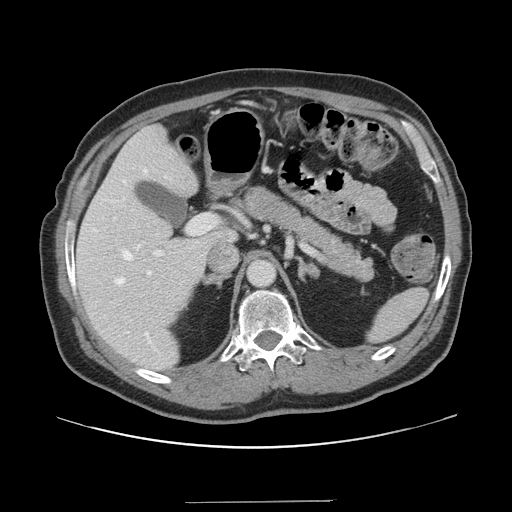
Contrast-enhanced abdominal CT, one axial slice. Position 91 of 151 along the scan axis. 120 kVp. Soft-tissue window (W 400 / L 40 HU). 2.5 mm slice thickness. 512 × 512 image matrix, field of view 399 × 399 mm. Male patient, age 63 years. From the clinical record (not read from this slice): diagnosis: colorectal cancer liver metastases, imaged before liver resection; multiple liver metastases: no; largest metastasis: 2.1 cm; disease in both lobes: no.
Structures marked on this image (expert manual segmentation):
- hepatic veins: box from (x=115, y=168) to (x=158, y=352) px
- liver: (x=77, y=126)–(x=235, y=372)
- planned liver remnant (the part of the liver to remain after resection): (x=76, y=126)–(x=235, y=371)
- portal vein (with intrahepatic branches): (x=153, y=214)–(x=217, y=257)